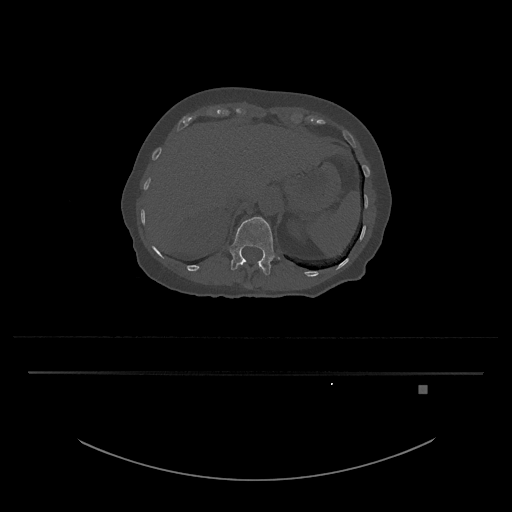
CT including the spine, one axial slice; slice 570 of 797 in the series (ordered by position); reconstruction kernel Br40s/3; bone window (W 1800 / L 400 HU); 0.5 mm slice thickness; 512 × 512 image matrix, field of view 500 × 500 mm. Female patient, age 57 years. Case-level facts recorded for this patient, not image findings: primary cancer: cervical.
Annotated regions visible in this slice (semi-automatically segmented with operator editing):
- L1 vertebra: bounding box (x1, y1, x2, y2) in pixels: (229, 217, 280, 275)
- T12 vertebra: (238, 262, 264, 273)